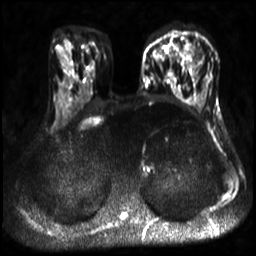
Breast MRI, one axial slice. Position 14 of 30 along the scan axis. Diffusion-weighted series; image 2 of 4 stored at this slice position (different b-values; order by instance number). 3 T. 4 mm slice thickness. 256 × 256 image matrix, field of view 320 × 320 mm. Female patient.
Outlined on this slice (outlined manually by an expert reader):
- tumour on diffusion-weighted imaging: bounding box <183,40,196,54> (left, top, right, bottom; pixels)